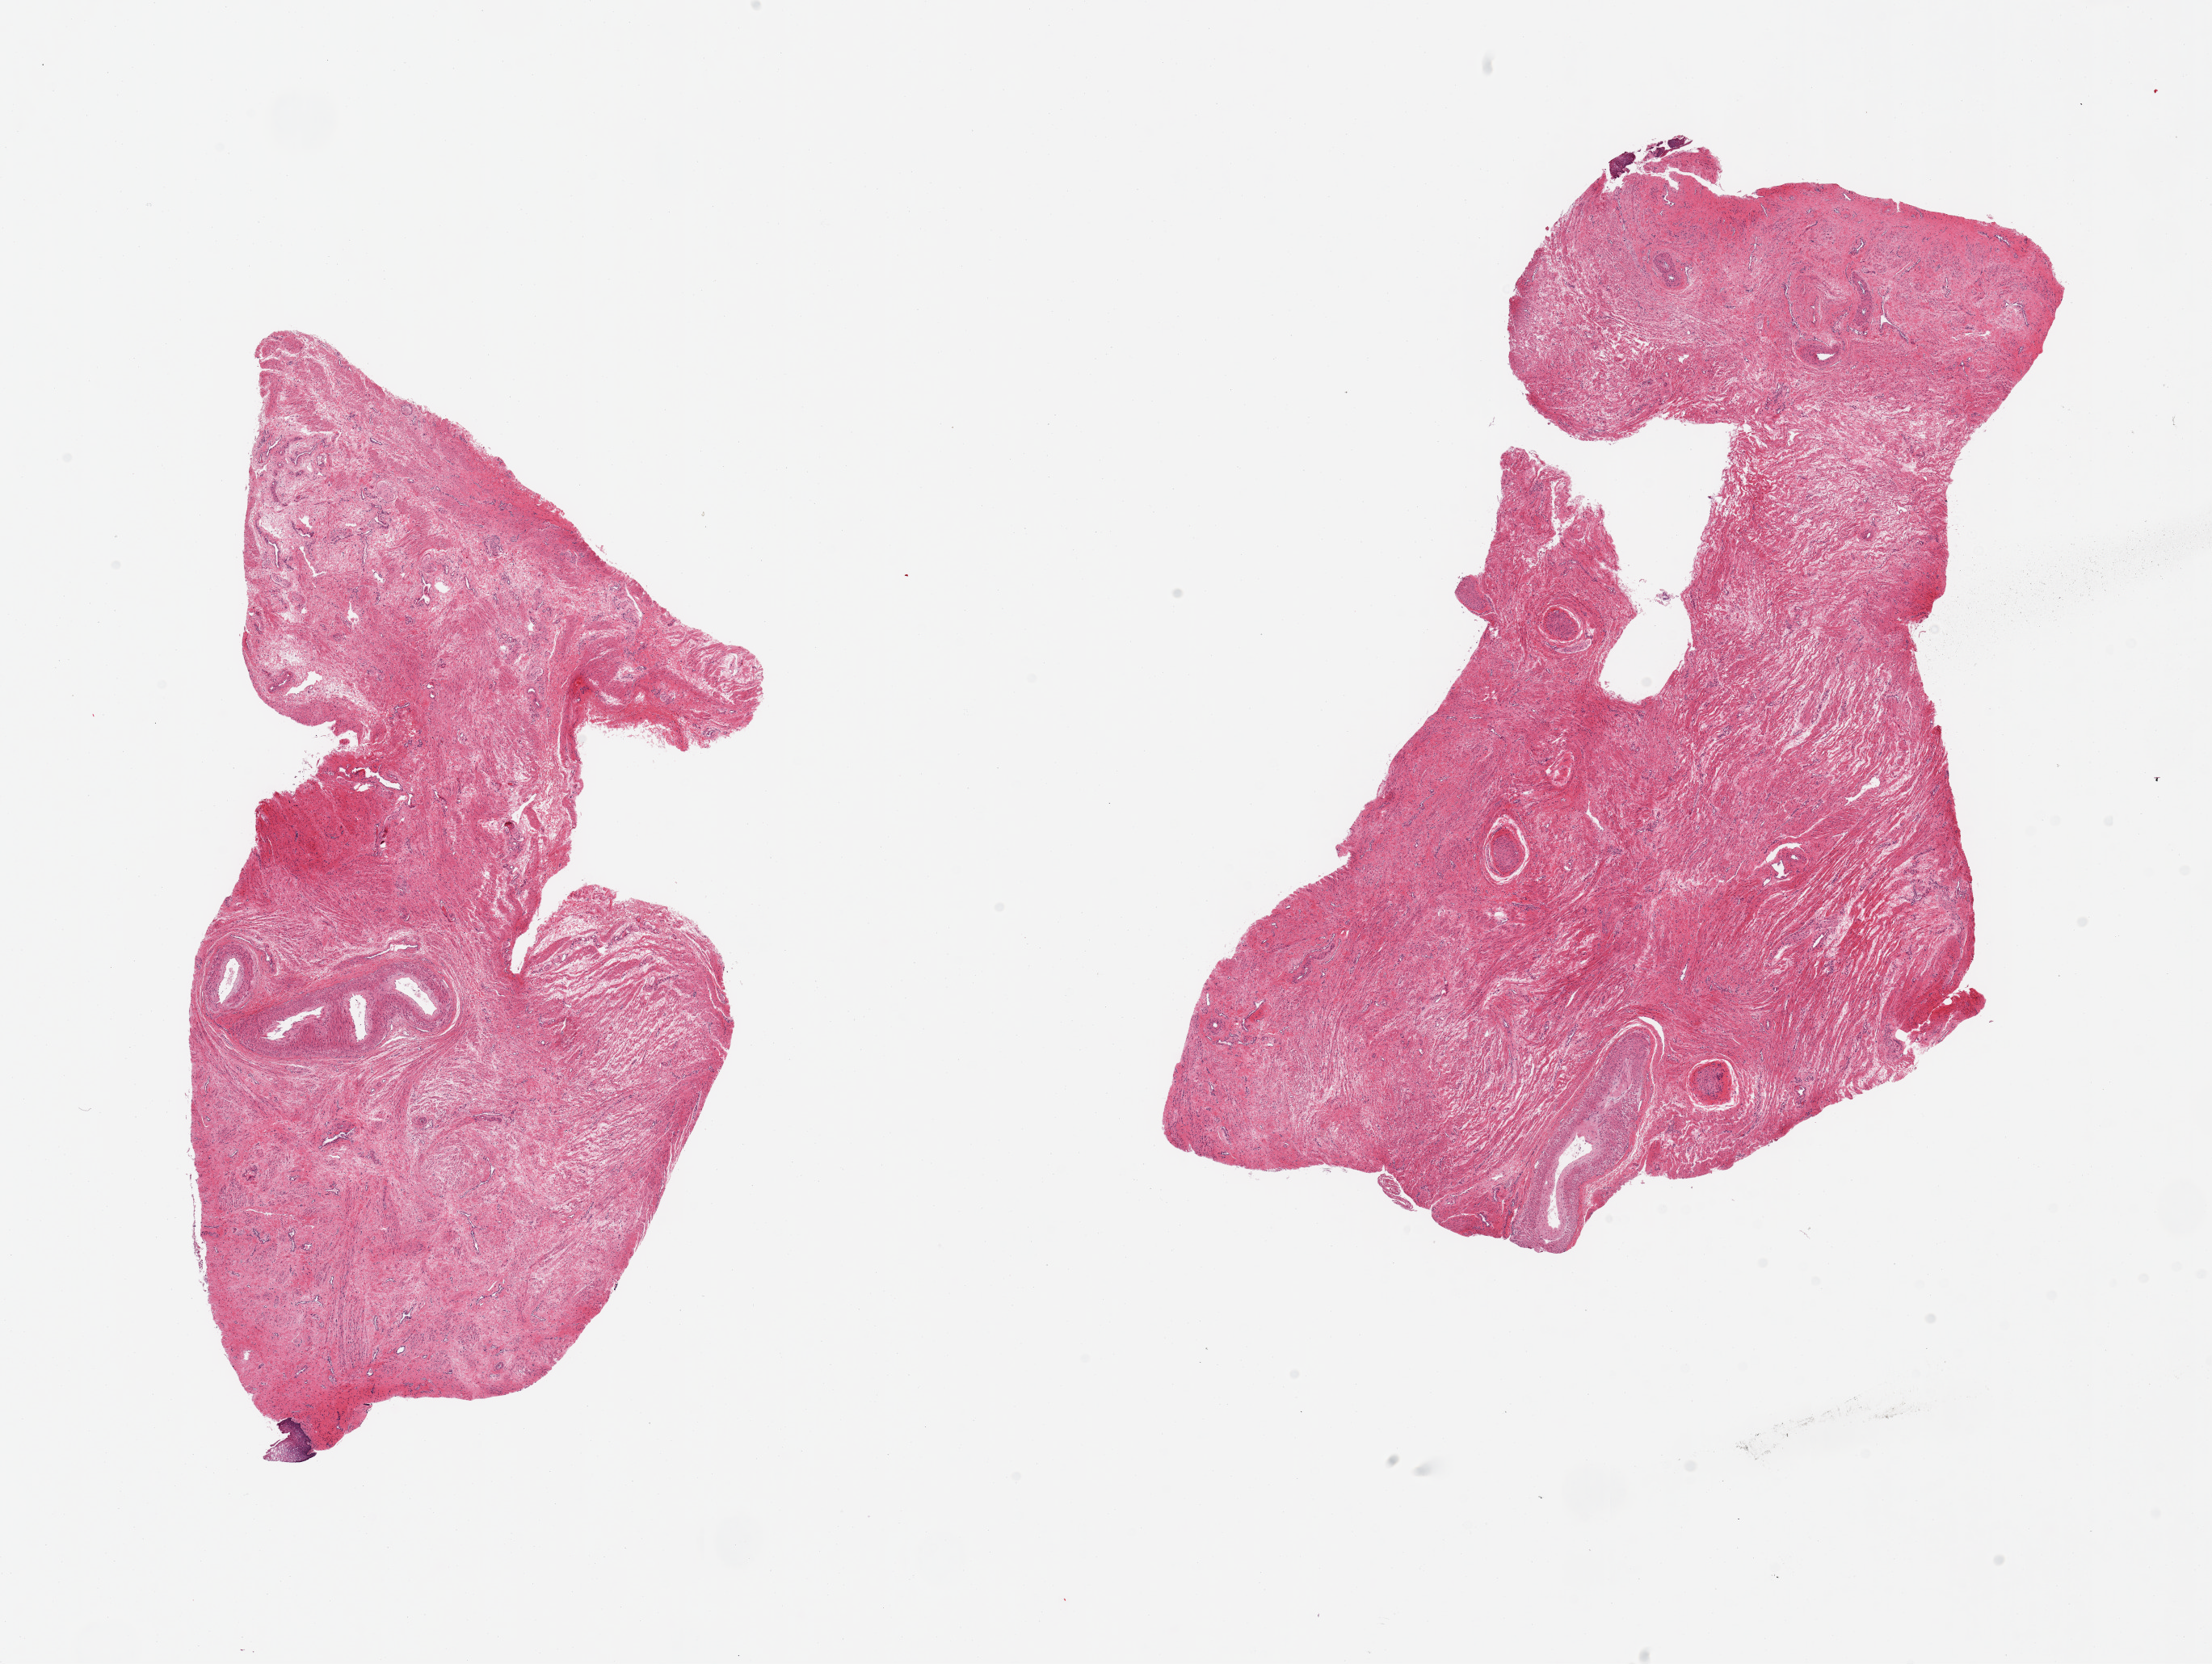
Haematoxylin and eosin whole-slide image — low-resolution overview of the scanned area, about 21.7 x 16.3 mm (slide scanned at 20x), PAXgene-fixed paraffin-embedded (PFPE) section, target tissue: uterus, tissue donor sample. Female donor.
Review note (as recorded): 2 pieces; portion of ectocervix (target is corpus to include endometrium).